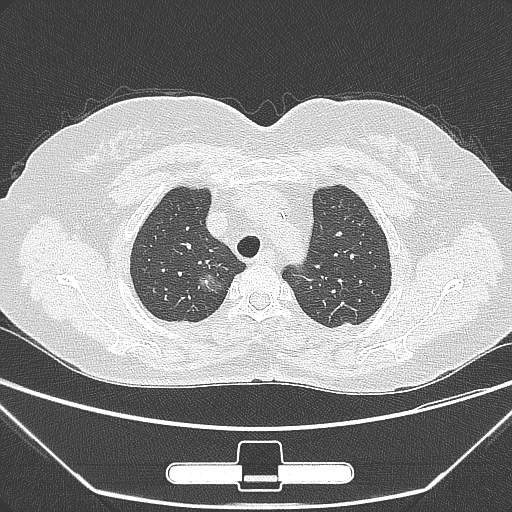
Chest CT, one axial slice; slice 228 of 275 in the series (ordered by position); 120 kVp; lung window (W 1500 / L -600 HU); 1 mm slice thickness; 512 × 512 image matrix, field of view 356 × 356 mm. Patient: female, 63 years. From the clinical record (not read from this slice): clinical TNM (as recorded): T1a N0 M0.
Structures marked on this image (bounding box drawn by a radiologist):
- lung tumour (recorded histology: adenocarcinoma): bounding box (x1, y1, x2, y2) in pixels: (195, 267, 223, 293)